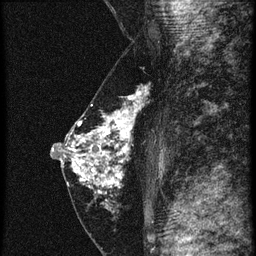
Breast MRI (dynamic contrast-enhanced), one sagittal slice. Position 30 of 60 along the scan axis. 4 images stored at this slice position (order not interpretable as contrast timing). 1.5 T. TE 4.2 ms, TR 20.4 ms. 1.5 mm slice thickness. 256 × 256 image matrix, field of view 180 × 180 mm. Female patient, age 46 years. Case-level facts recorded for this patient, not image findings: setting: breast cancer imaged before/during neoadjuvant chemotherapy; receptor status: triple-negative.
Structures marked on this image (semi-automatically segmented with operator editing):
- analysis volume of interest (the breast-tissue region the enhancement analysis was run in; not a lesion): bounding box <67,84,151,201> (left, top, right, bottom; pixels)
- tumour enhancement mask (voxels above the 90 % enhancement threshold inside the analysis volume of interest): <68,94,141,193>